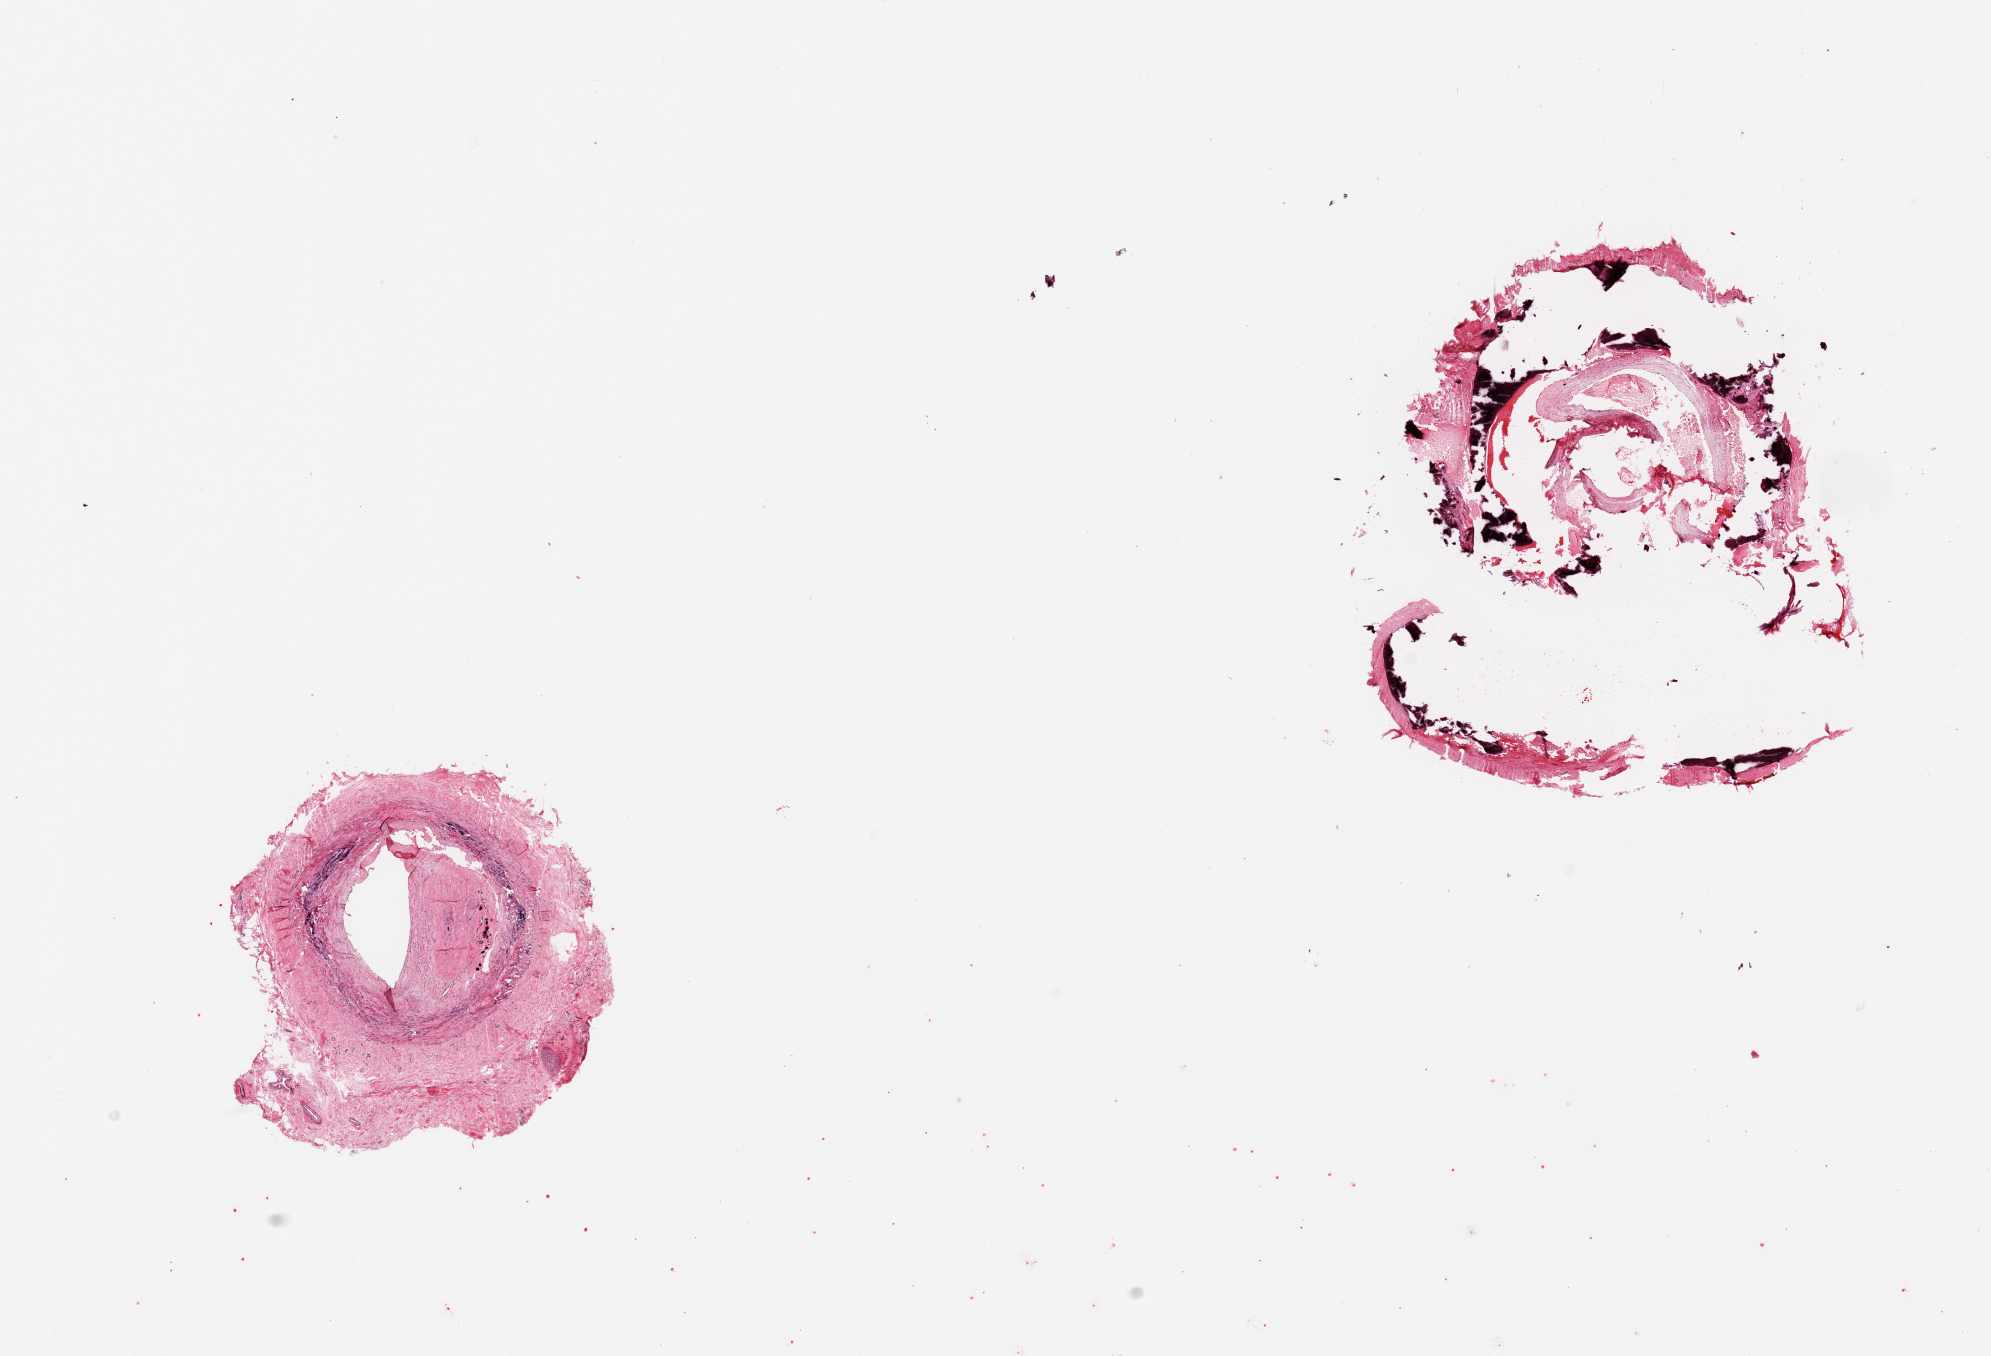
Whole-slide image, hematoxylin and eosin (H&E) stain, low-resolution overview of the scanned area, about 15.8 x 10.7 mm. PAXgene-fixed paraffin-embedded (PFPE) section. Sampled site (target tissue): tibial artery. Donor tissue sample. Donor: male.
Reviewer comment on this tissue sample: 2 pieces; 1 piece heavily calcified & fragmented (useless); other has 50% occlusive sclerotic partly calcified plaque; little normal tissue remains.